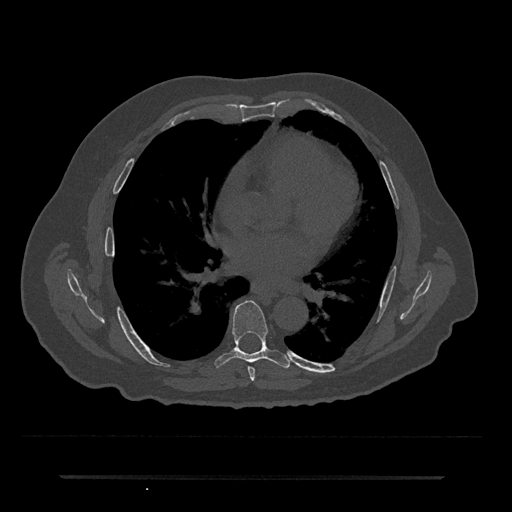
CT including the spine, one axial slice; slice 392 of 797 in the series (ordered by position); 120 kVp; bone window (W 1800 / L 400 HU); 0.5 mm slice thickness; 512 × 512 image matrix, field of view 437 × 437 mm. Male patient, age 69 years. Case-level facts recorded for this patient, not image findings: primary cancer: prostate.
Structures marked on this image (semi-automatic segmentation, software-assisted and operator-edited):
- T6 vertebra: bounding box <248,366,255,381> (left, top, right, bottom; pixels)
- T7 vertebra: <215,300,290,368>